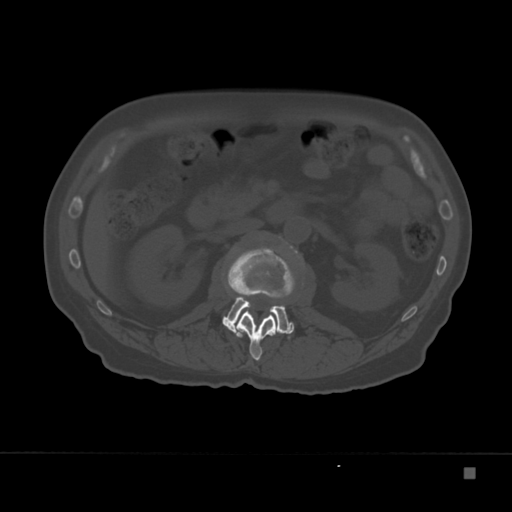
CT including the spine, one axial slice. Position 100 of 332 along the scan axis. Reconstruction kernel Br40s. 120 kVp. Bone window (W 1800 / L 400 HU). 512 × 512 image matrix, field of view 389 × 389 mm. Male patient, age 72 years. From the clinical record (not read from this slice): primary cancer: skeletal.
Outlined on this slice (semi-automatically segmented with operator editing):
- L1 vertebra: bounding box [x1, y1, x2, y2] px = [227, 246, 295, 361]
- L2 vertebra: [222, 295, 295, 334]